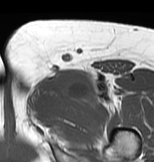
MRI of an extremity soft-tissue mass, one axial slice; slice 45 of 83 in the series (ordered by position); MR volume resampled by the dataset authors to the PET/CT grid (not the native acquisition matrix); 3.27 mm slice thickness; 154 × 162 image matrix. Female patient. Case-level facts recorded for this patient, not image findings: histological type: myxofibrosarcoma; grade: intermediate; site of the primary tumour: left thigh.
Structures marked on this image (expert contour drawn on MRI and transferred to this co-registered scan by the dataset authors):
- gross tumour volume including surrounding oedema: bounding box (x1, y1, x2, y2) in pixels: (26, 70, 127, 117)
- gross tumour volume (mass): (56, 70, 88, 99)